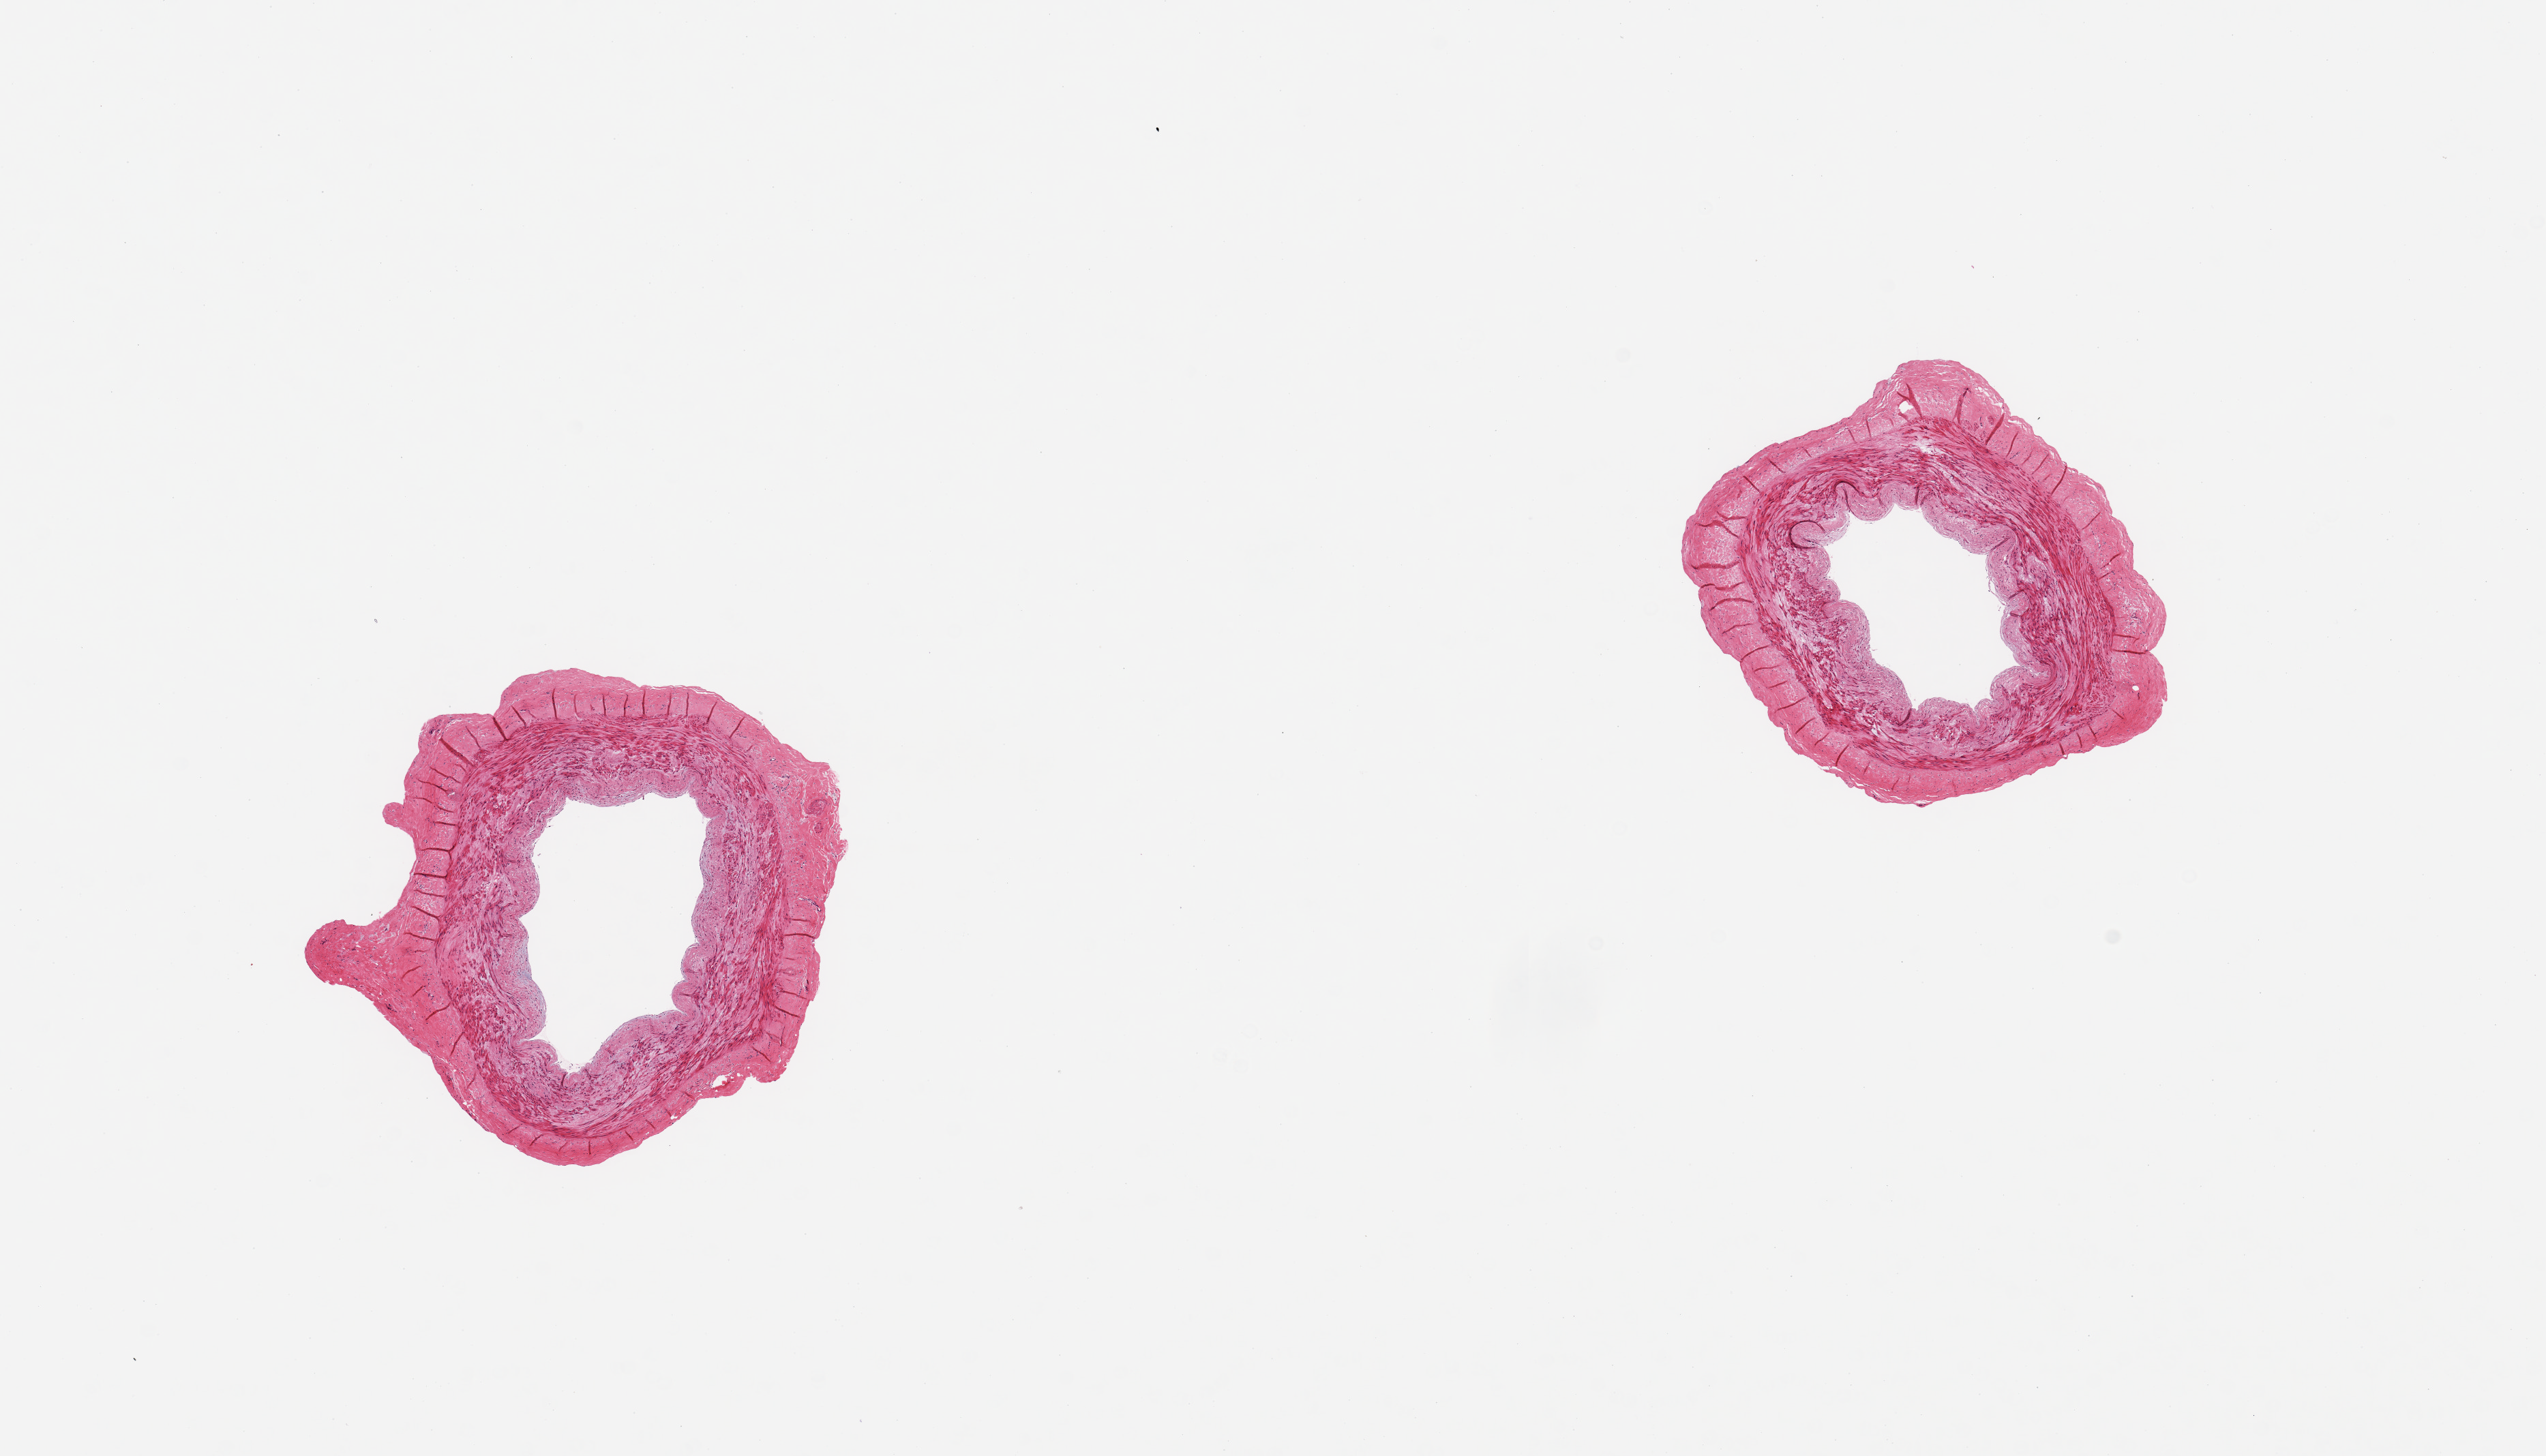
Hematoxylin and eosin (H&E) whole-slide image — a low-resolution overview of the entire scanned area, about 14.8 x 8.4 mm (slide scanned at 20x); PAXgene-fixed, paraffin-embedded tissue; target tissue: tibial artery; tissue donor sample. Donor: female.
- pathologist's review note for this sample: 2 pieces; early atherosis; lumina open